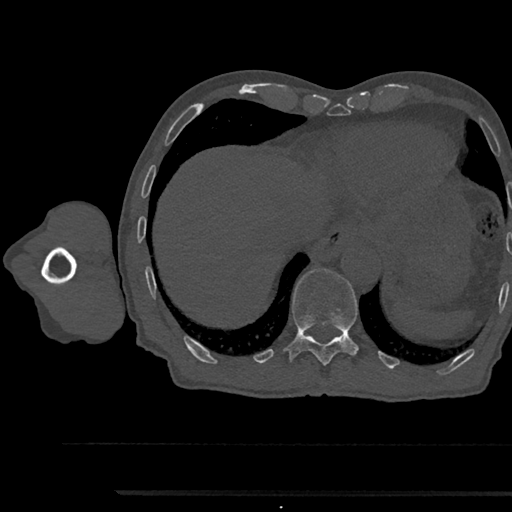
CT including the spine, one axial slice; slice 786 of 797 in the series (ordered by position); bone window (W 1800 / L 400 HU); 0.5 mm slice thickness; 512 × 512 image matrix, field of view 367 × 367 mm. Patient: male, 79 years. From the clinical record (not read from this slice): primary cancer: prostate.
Structures marked on this image (semi-automatically segmented with operator editing):
- T11 vertebra: bounding box <287,268,358,366> (left, top, right, bottom; pixels)